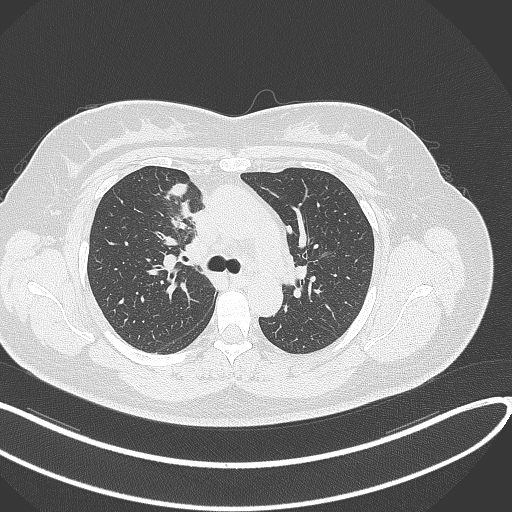
Chest CT, one axial slice; slice 189 of 303 in the series (ordered by position); 120 kVp; lung window (W 1500 / L -600 HU); 1 mm slice thickness; 512 × 512 image matrix. Patient: female, 46 years. From the clinical record (not read from this slice): clinical TNM (as recorded): T2a N1 M0.
Outlined on this slice (bounding box drawn by a radiologist):
- lung tumour (recorded histology: adenocarcinoma): box from (x=158, y=179) to (x=194, y=222) px